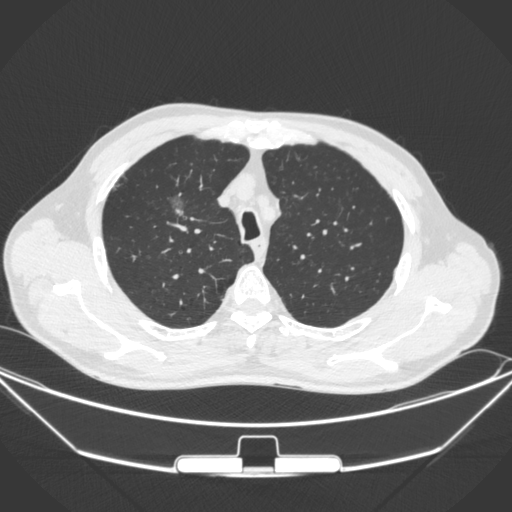
Chest CT, one axial slice; position 269 of 355 along the scan axis; lung window (W 1500 / L -600 HU); 1 mm slice thickness; 512 × 512 image matrix, field of view 399 × 399 mm. Patient: male, 67 years. Case-level facts recorded for this patient, not image findings: clinical TNM (as recorded): T1c N0 M0; histopathological grade: G2.
Annotated regions visible in this slice (rectangle marked by the reading radiologist):
- lung tumour (recorded histology: adenocarcinoma): bounding box [x1, y1, x2, y2] px = [164, 190, 200, 230]